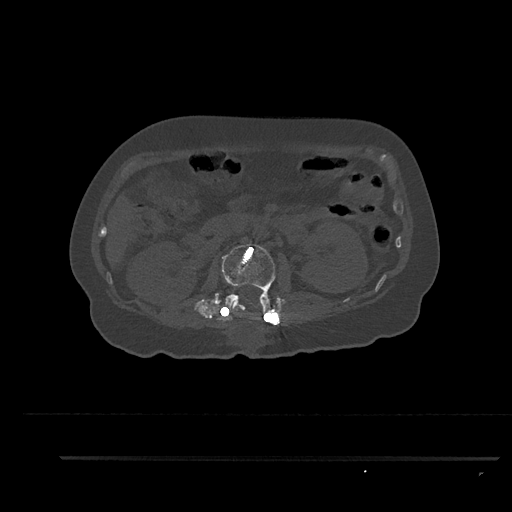
CT including the spine, one axial slice; position 180 of 797 along the scan axis; reconstruction kernel Br40s/3; 120 kVp; bone window (W 1800 / L 400 HU); 0.5 mm slice thickness; 512 × 512 image matrix, field of view 408 × 408 mm. Female patient, age 44 years. From the clinical record (not read from this slice): primary cancer: renal.
Annotated regions visible in this slice (semi-automatic segmentation, software-assisted and operator-edited):
- L2 vertebra: bounding box (x1, y1, x2, y2) in pixels: (223, 242, 276, 321)